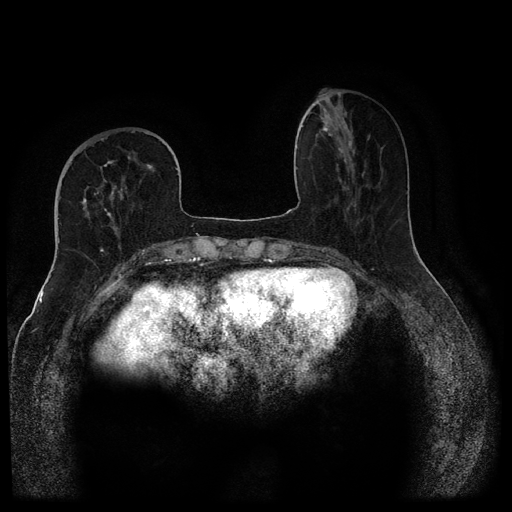
Breast MRI (dynamic contrast-enhanced, multi-phase), one axial slice; slice 38 of 116 in the series (ordered by position); dynamic contrast-enhanced series, time point 2 of 5 at this slice position (early post-contrast); 1.5 T; TE 2.6 ms, TR 5.4 ms; 2 mm slice thickness; 512 × 512 image matrix, field of view 340 × 340 mm. Female patient, age 68 years.
Annotated regions visible in this slice (semi-automatic segmentation, software-assisted and operator-edited):
- breast lesion (labelled benign in the annotation): bounding box [x1, y1, x2, y2] px = [320, 117, 336, 137]